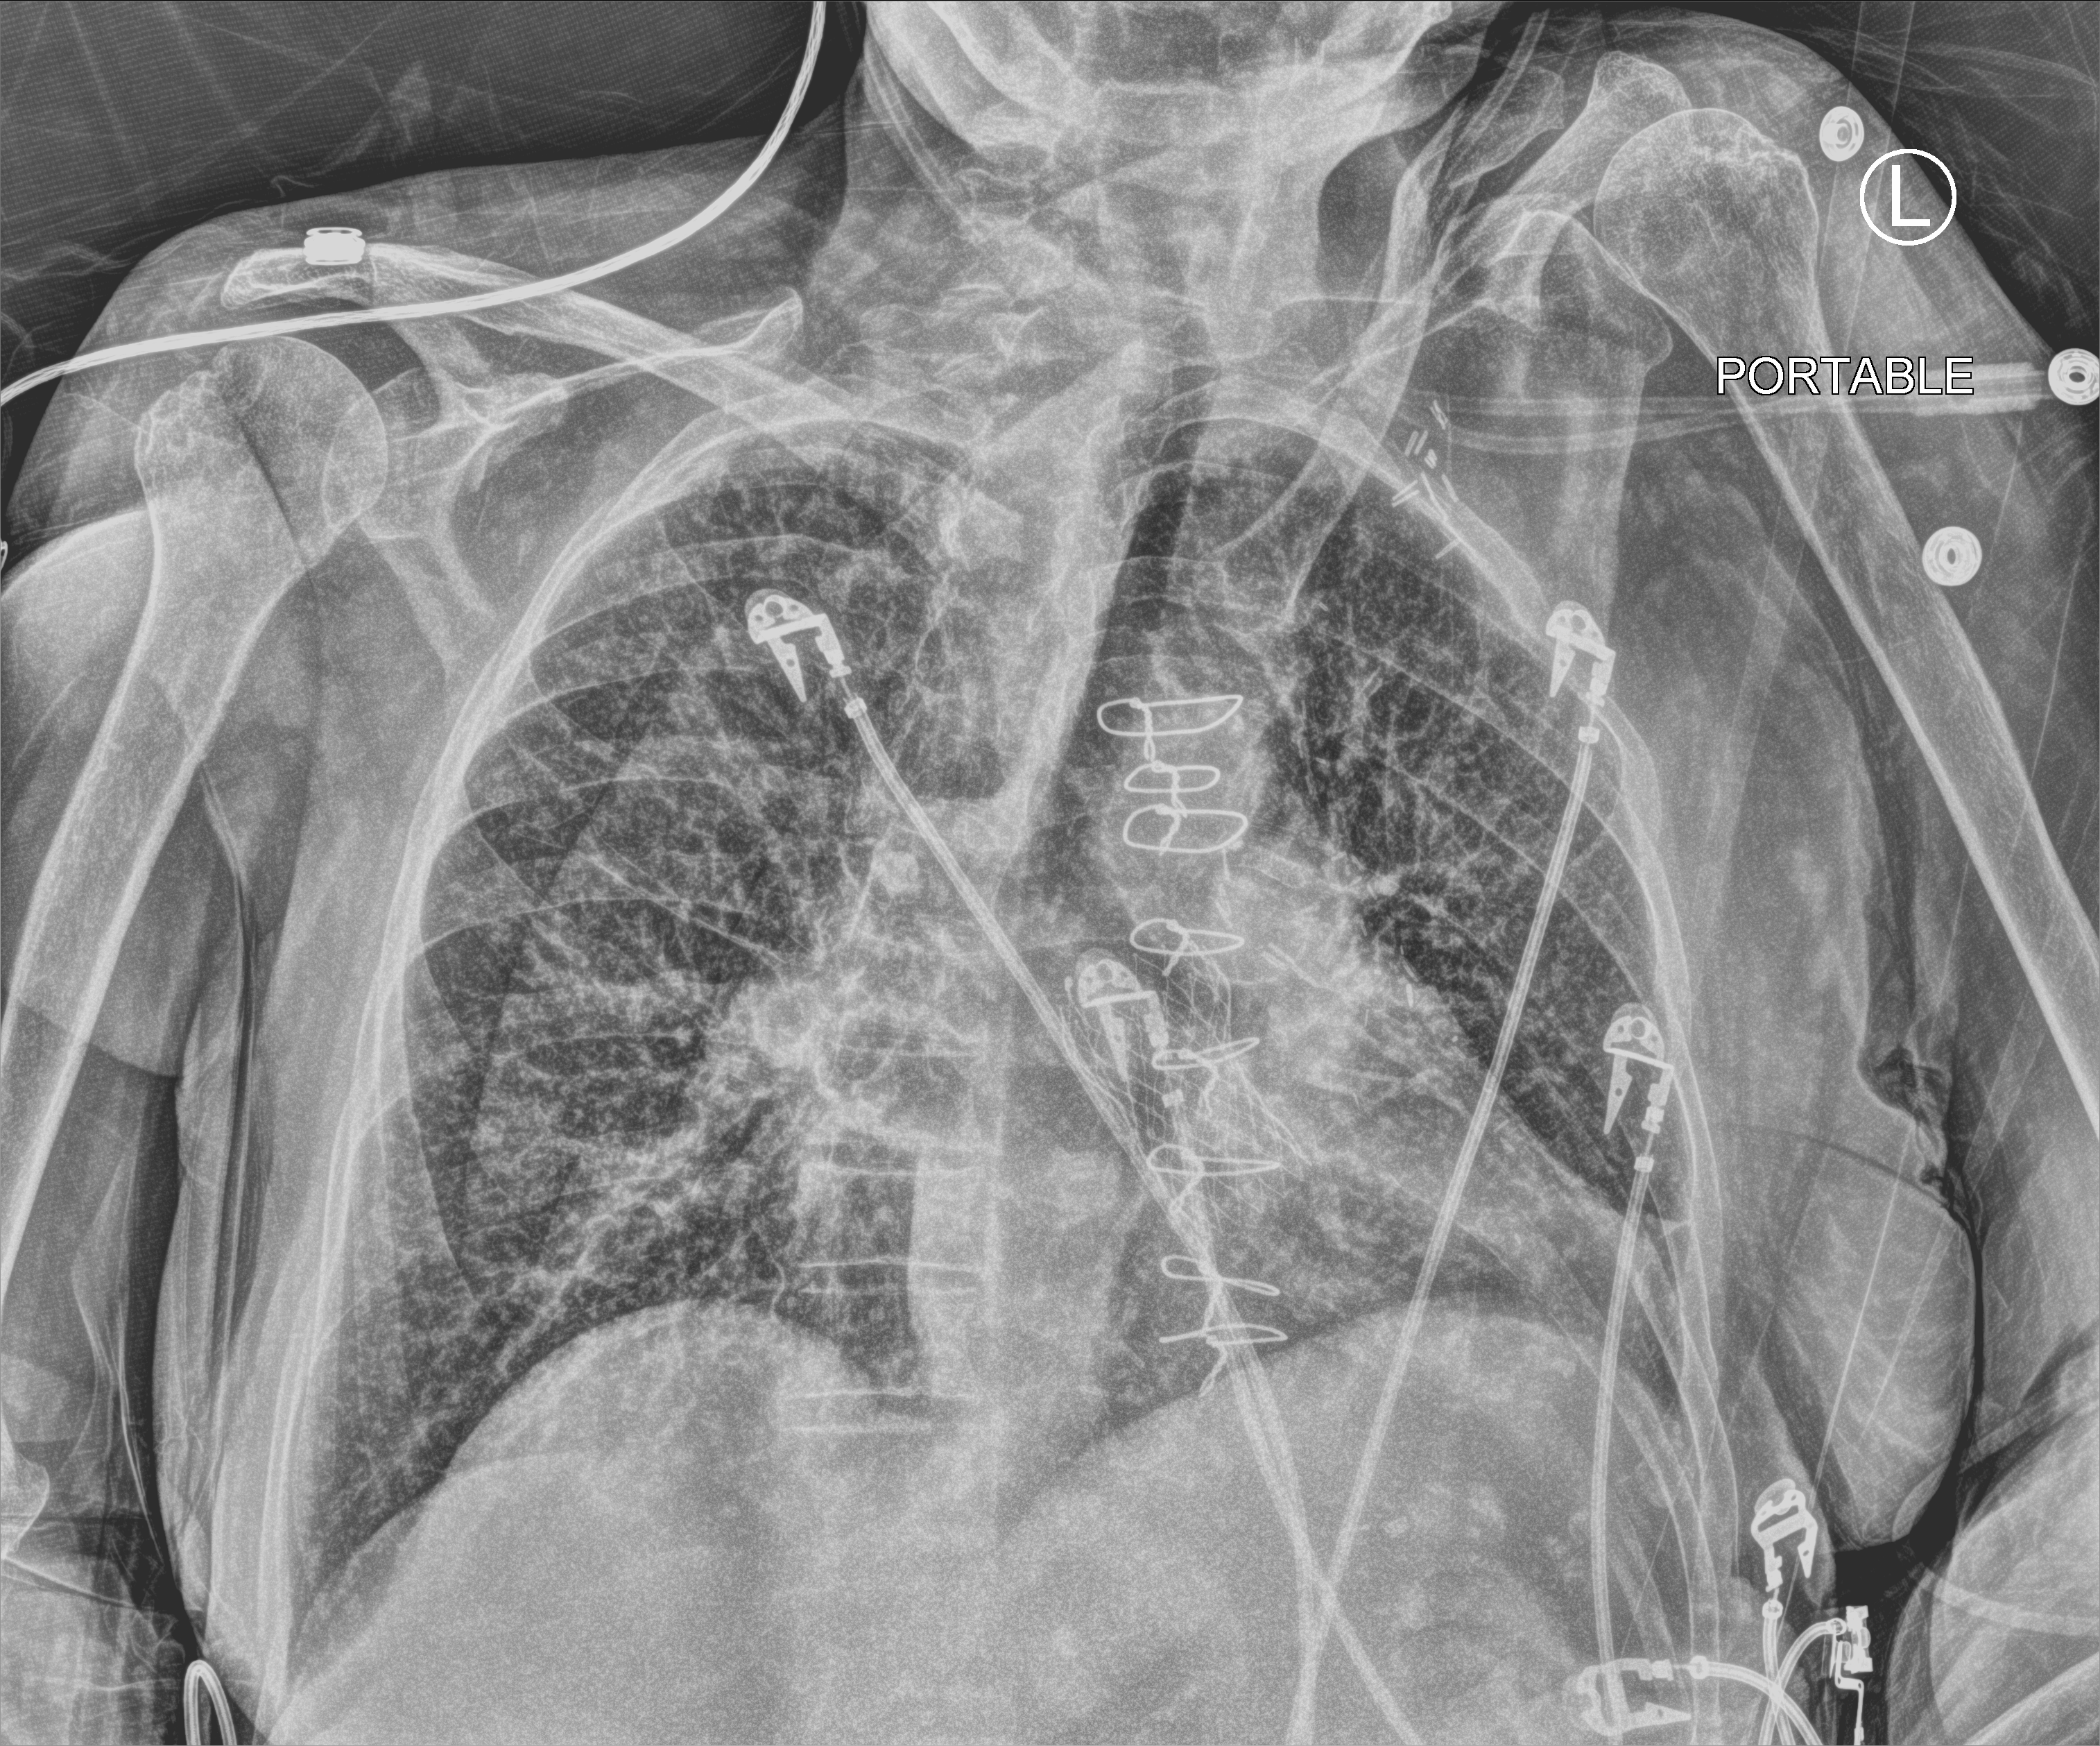
Portable chest radiograph, anteroposterior (AP) projection. Female patient hospitalised with COVID-19, age 75–90 years.
Admission-level facts for this patient (not findings on this image; timing relative to this image not recorded):
- COPD (admission record): yes